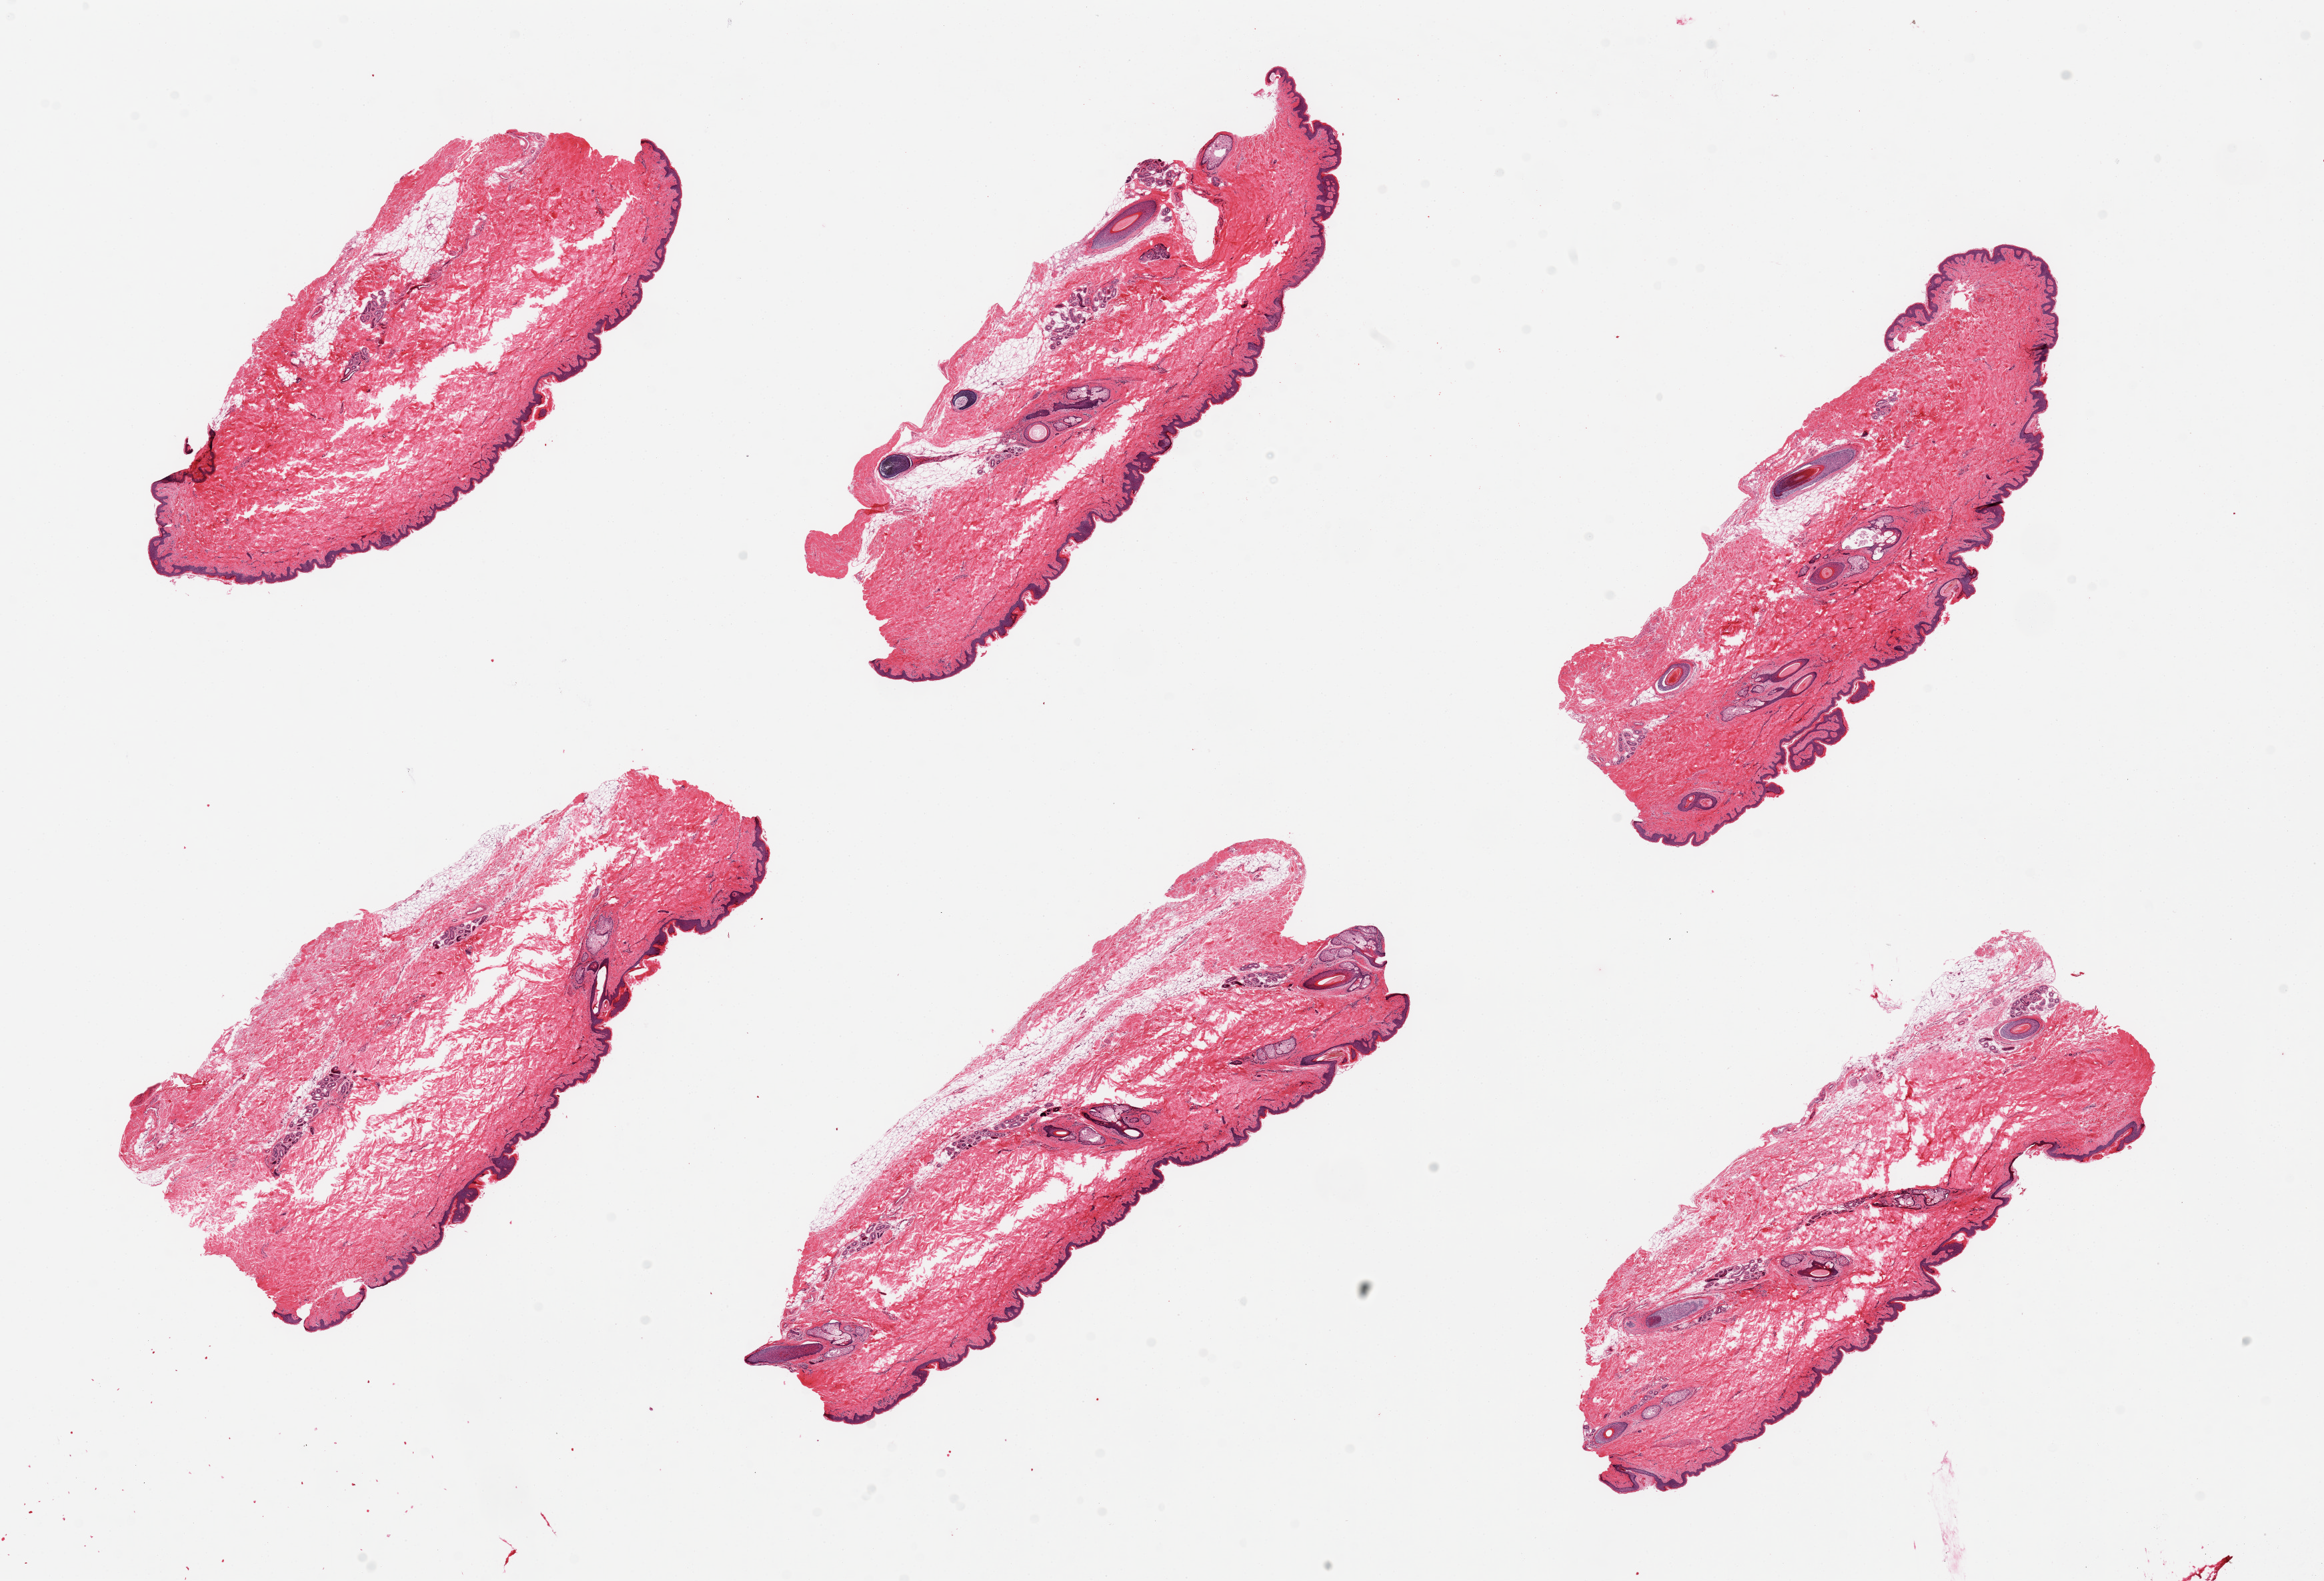
Digitized H&E-stained section, whole scanned area (about 27.6 x 18.8 mm) shown as a low-resolution overview, PAXgene-fixed paraffin-embedded (PFPE) section, target tissue: skin of suprapubic region, donor tissue sample. Donor: male.
Pathologist's review note for this sample: 6 pieces, few pieces include up to 5-10% fat, rare fungal elements.